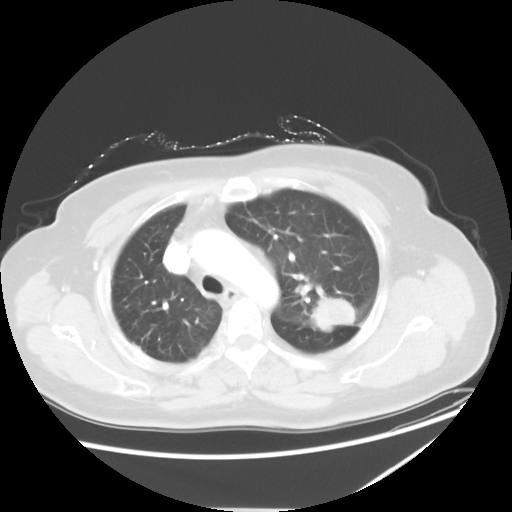
Chest CT, one axial slice; position 40 of 54 along the scan axis; reconstruction kernel STANDARD; 120 kVp; lung window (W 1500 / L -600 HU); 5 mm slice thickness; 512 × 512 image matrix. Female patient, age 61 years. Case-level facts recorded for this patient, not image findings: clinical TNM (as recorded): T1c N3 M1.
Structures marked on this image (rectangle marked by the reading radiologist):
- lung tumour (recorded histology: adenocarcinoma): bounding box [x1, y1, x2, y2] px = [303, 291, 359, 336]